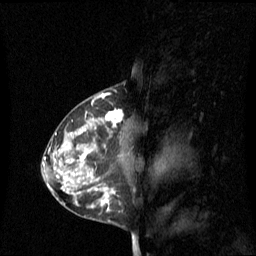
Breast MRI (dynamic contrast-enhanced), one sagittal slice. Position 38 of 60 along the scan axis. Dynamic contrast-enhanced series, image 2 of 3 at this slice position (ordered by acquisition). 1.5 T. TE 4.2 ms, TR 8.4 ms. 256 × 256 image matrix, field of view 240 × 240 mm. Female patient, age 42 years. From the clinical record (not read from this slice): setting: breast cancer imaged before/during neoadjuvant chemotherapy; receptor status: HR-positive, HER2-negative.
Outlined on this slice (semi-automatic segmentation, software-assisted and operator-edited):
- analysis volume of interest (the breast-tissue region the enhancement analysis was run in; not a lesion): bounding box (x1, y1, x2, y2) in pixels: (68, 108, 125, 201)
- tumour enhancement mask (voxels above the 70 % enhancement threshold inside the analysis volume of interest): (80, 110, 123, 201)